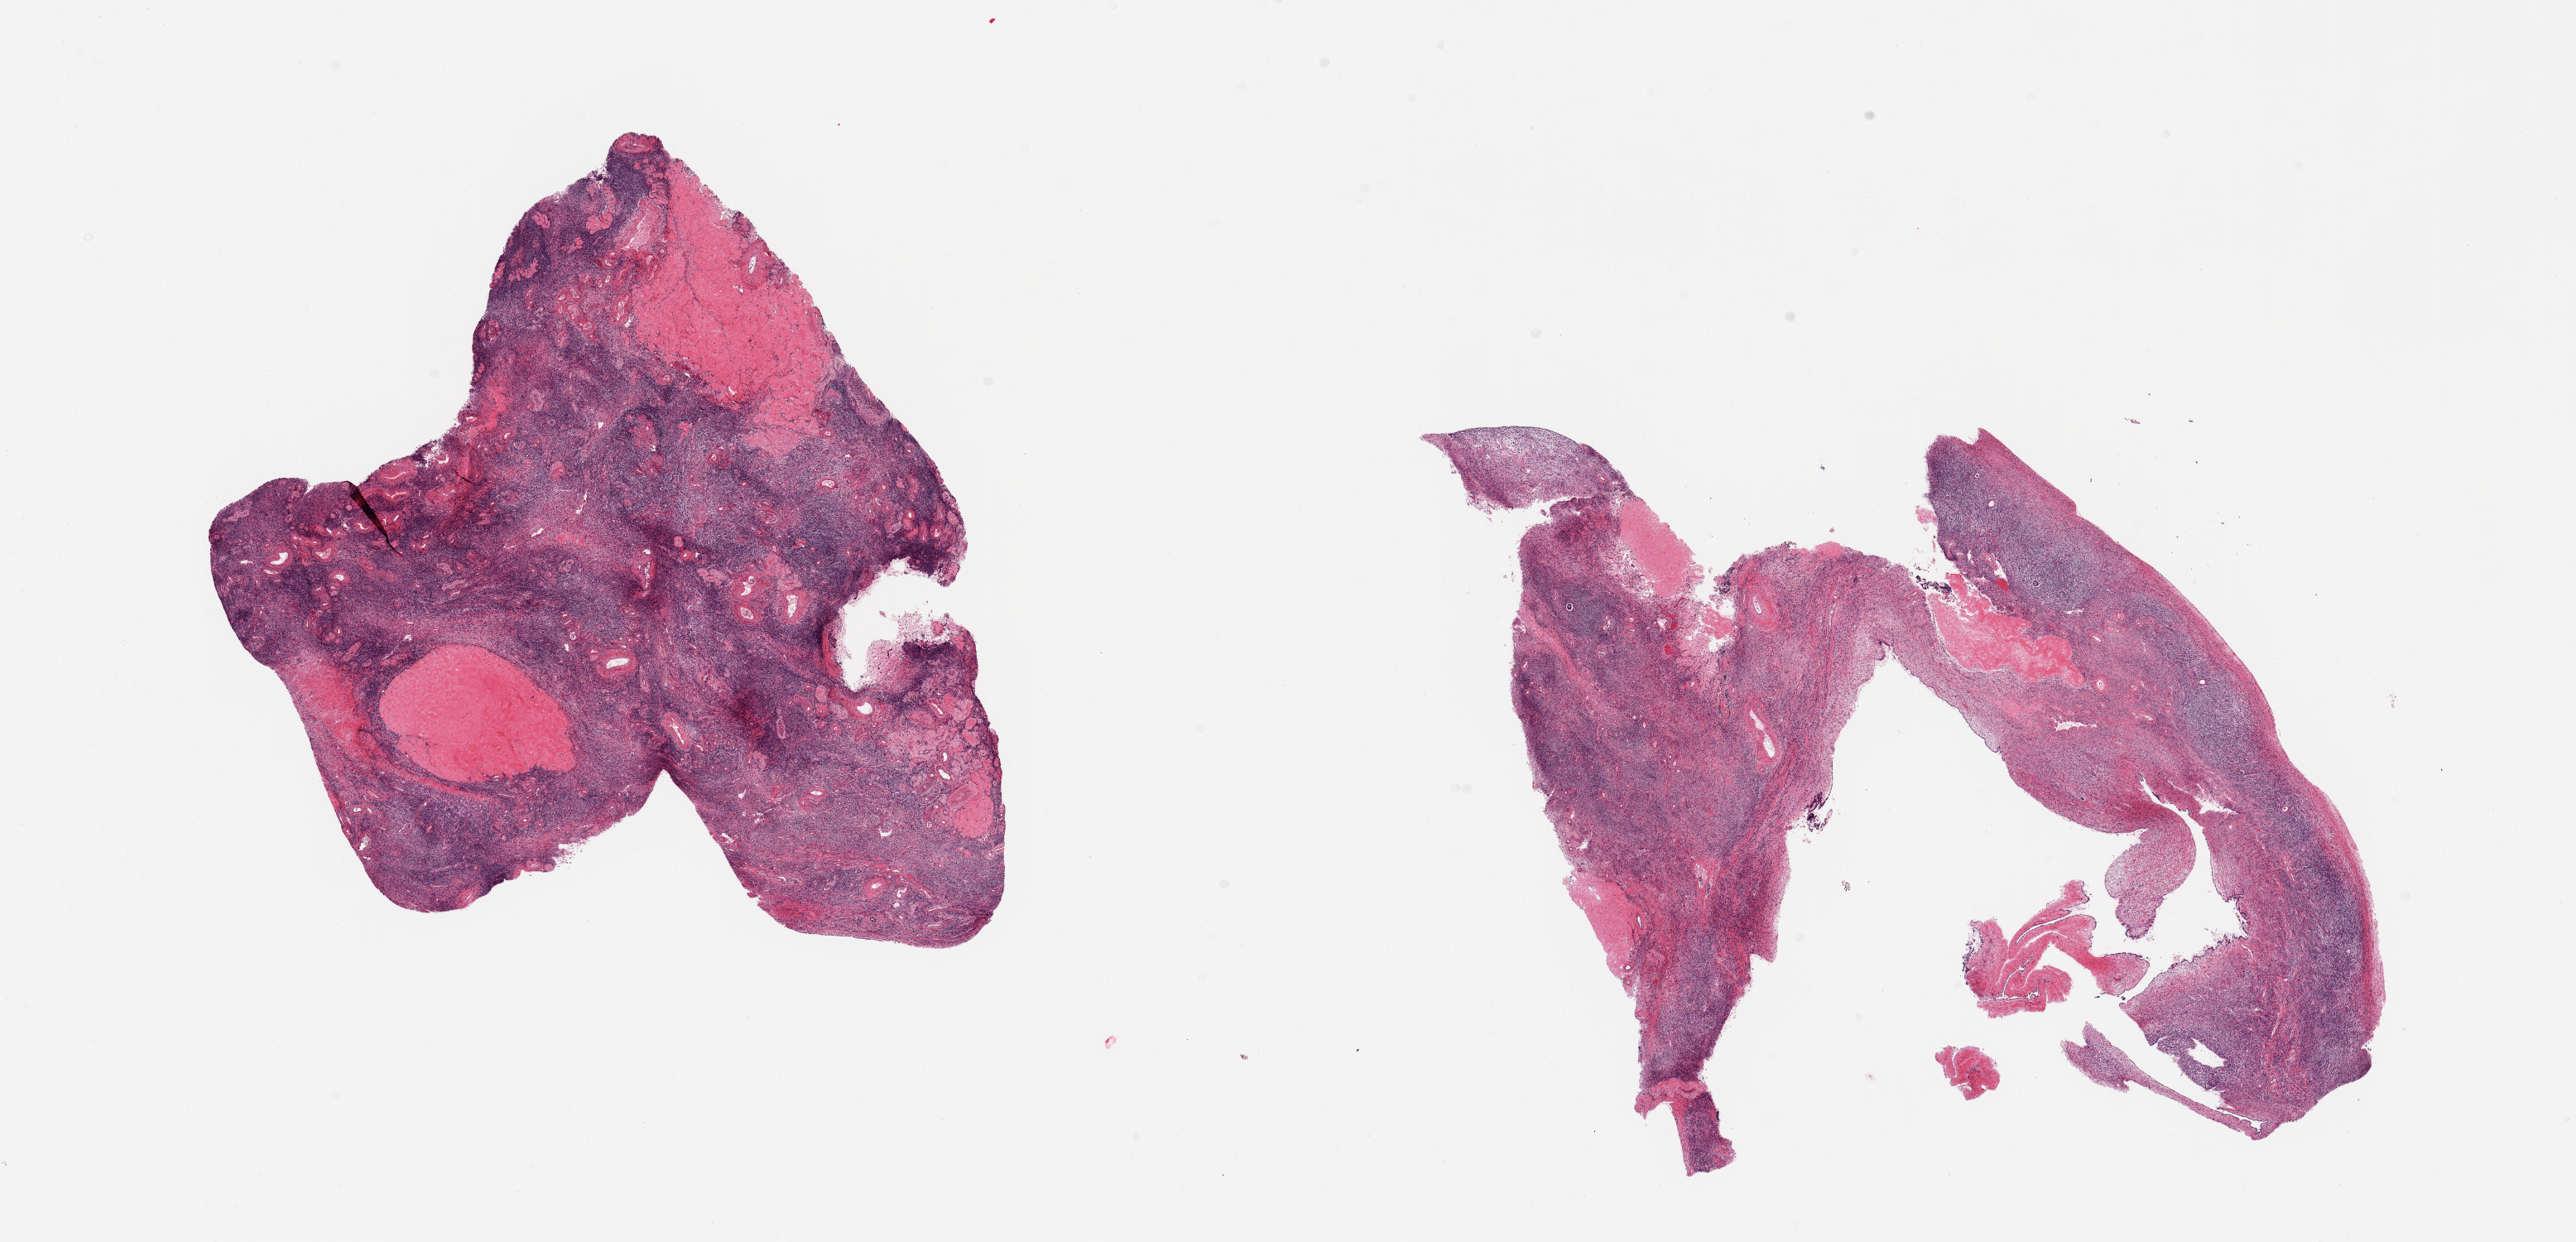
Whole-slide image, hematoxylin and eosin (H&E) stain — shown as a low-resolution overview of the whole scanned area (about 24.6 x 11.9 mm). PAXgene-fixed, paraffin-embedded tissue. Section of ovary (target tissue). Tissue donor sample. Donor: female.
- reviewer comment on this tissue sample: 2 pieces